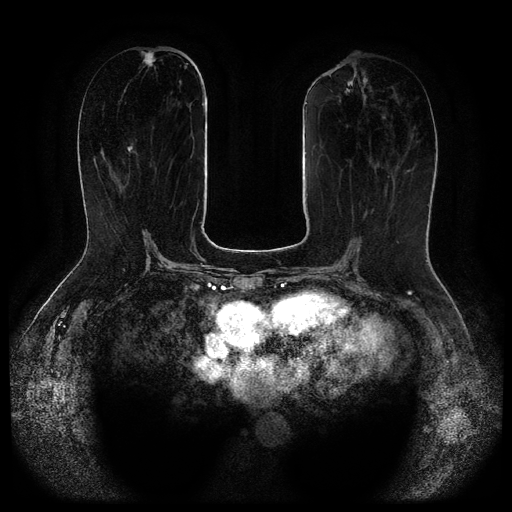
Breast MRI (dynamic contrast-enhanced, multi-phase), one axial slice. Position 41 of 116 along the scan axis. Dynamic contrast-enhanced series, time point 2 of 5 at this slice position (early post-contrast). 1.5 T. TE 2.6 ms, TR 5.3 ms. 2.1 mm slice thickness. 512 × 512 image matrix. Female patient, age 65 years.
Annotated regions visible in this slice (semi-automatically segmented with operator editing):
- breast lesion (labelled 'tumour' in the annotation; benign lesions carry a separate 'benign' label): bounding box [x1, y1, x2, y2] px = [142, 51, 155, 67]